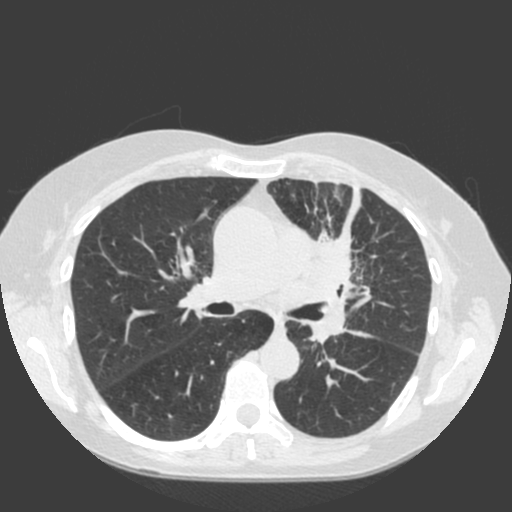
Low-dose screening chest CT, axial slice; baseline annual screen; lung window (W 1500 / L -600 HU); 2 mm slice thickness; slice 71 of 184 in the series; 512 × 512 image matrix. Female participant, aged 66 years at enrolment. Current smoker at enrolment.
- Lesion marked by an expert reader, bounding box <277,206,401,318> (left, top, right, bottom; pixels).
- The exam's reader record, not a measurement of the box and not confirmed to be the same lesion: non-calcified nodule or mass ≥4 mm, left upper lobe, 61 × 45 mm, spiculated (stellate) margins, soft tissue attenuation.
- Lung cancer was diagnosed 19 days after this screen: squamous cell carcinoma, keratinizing, NOS, left upper lobe, left hilum, mediastinum, left main stem bronchus, other location, poorly differentiated (G3), stage IIIB (AJCC 6th edition), 60 mm at pathology.